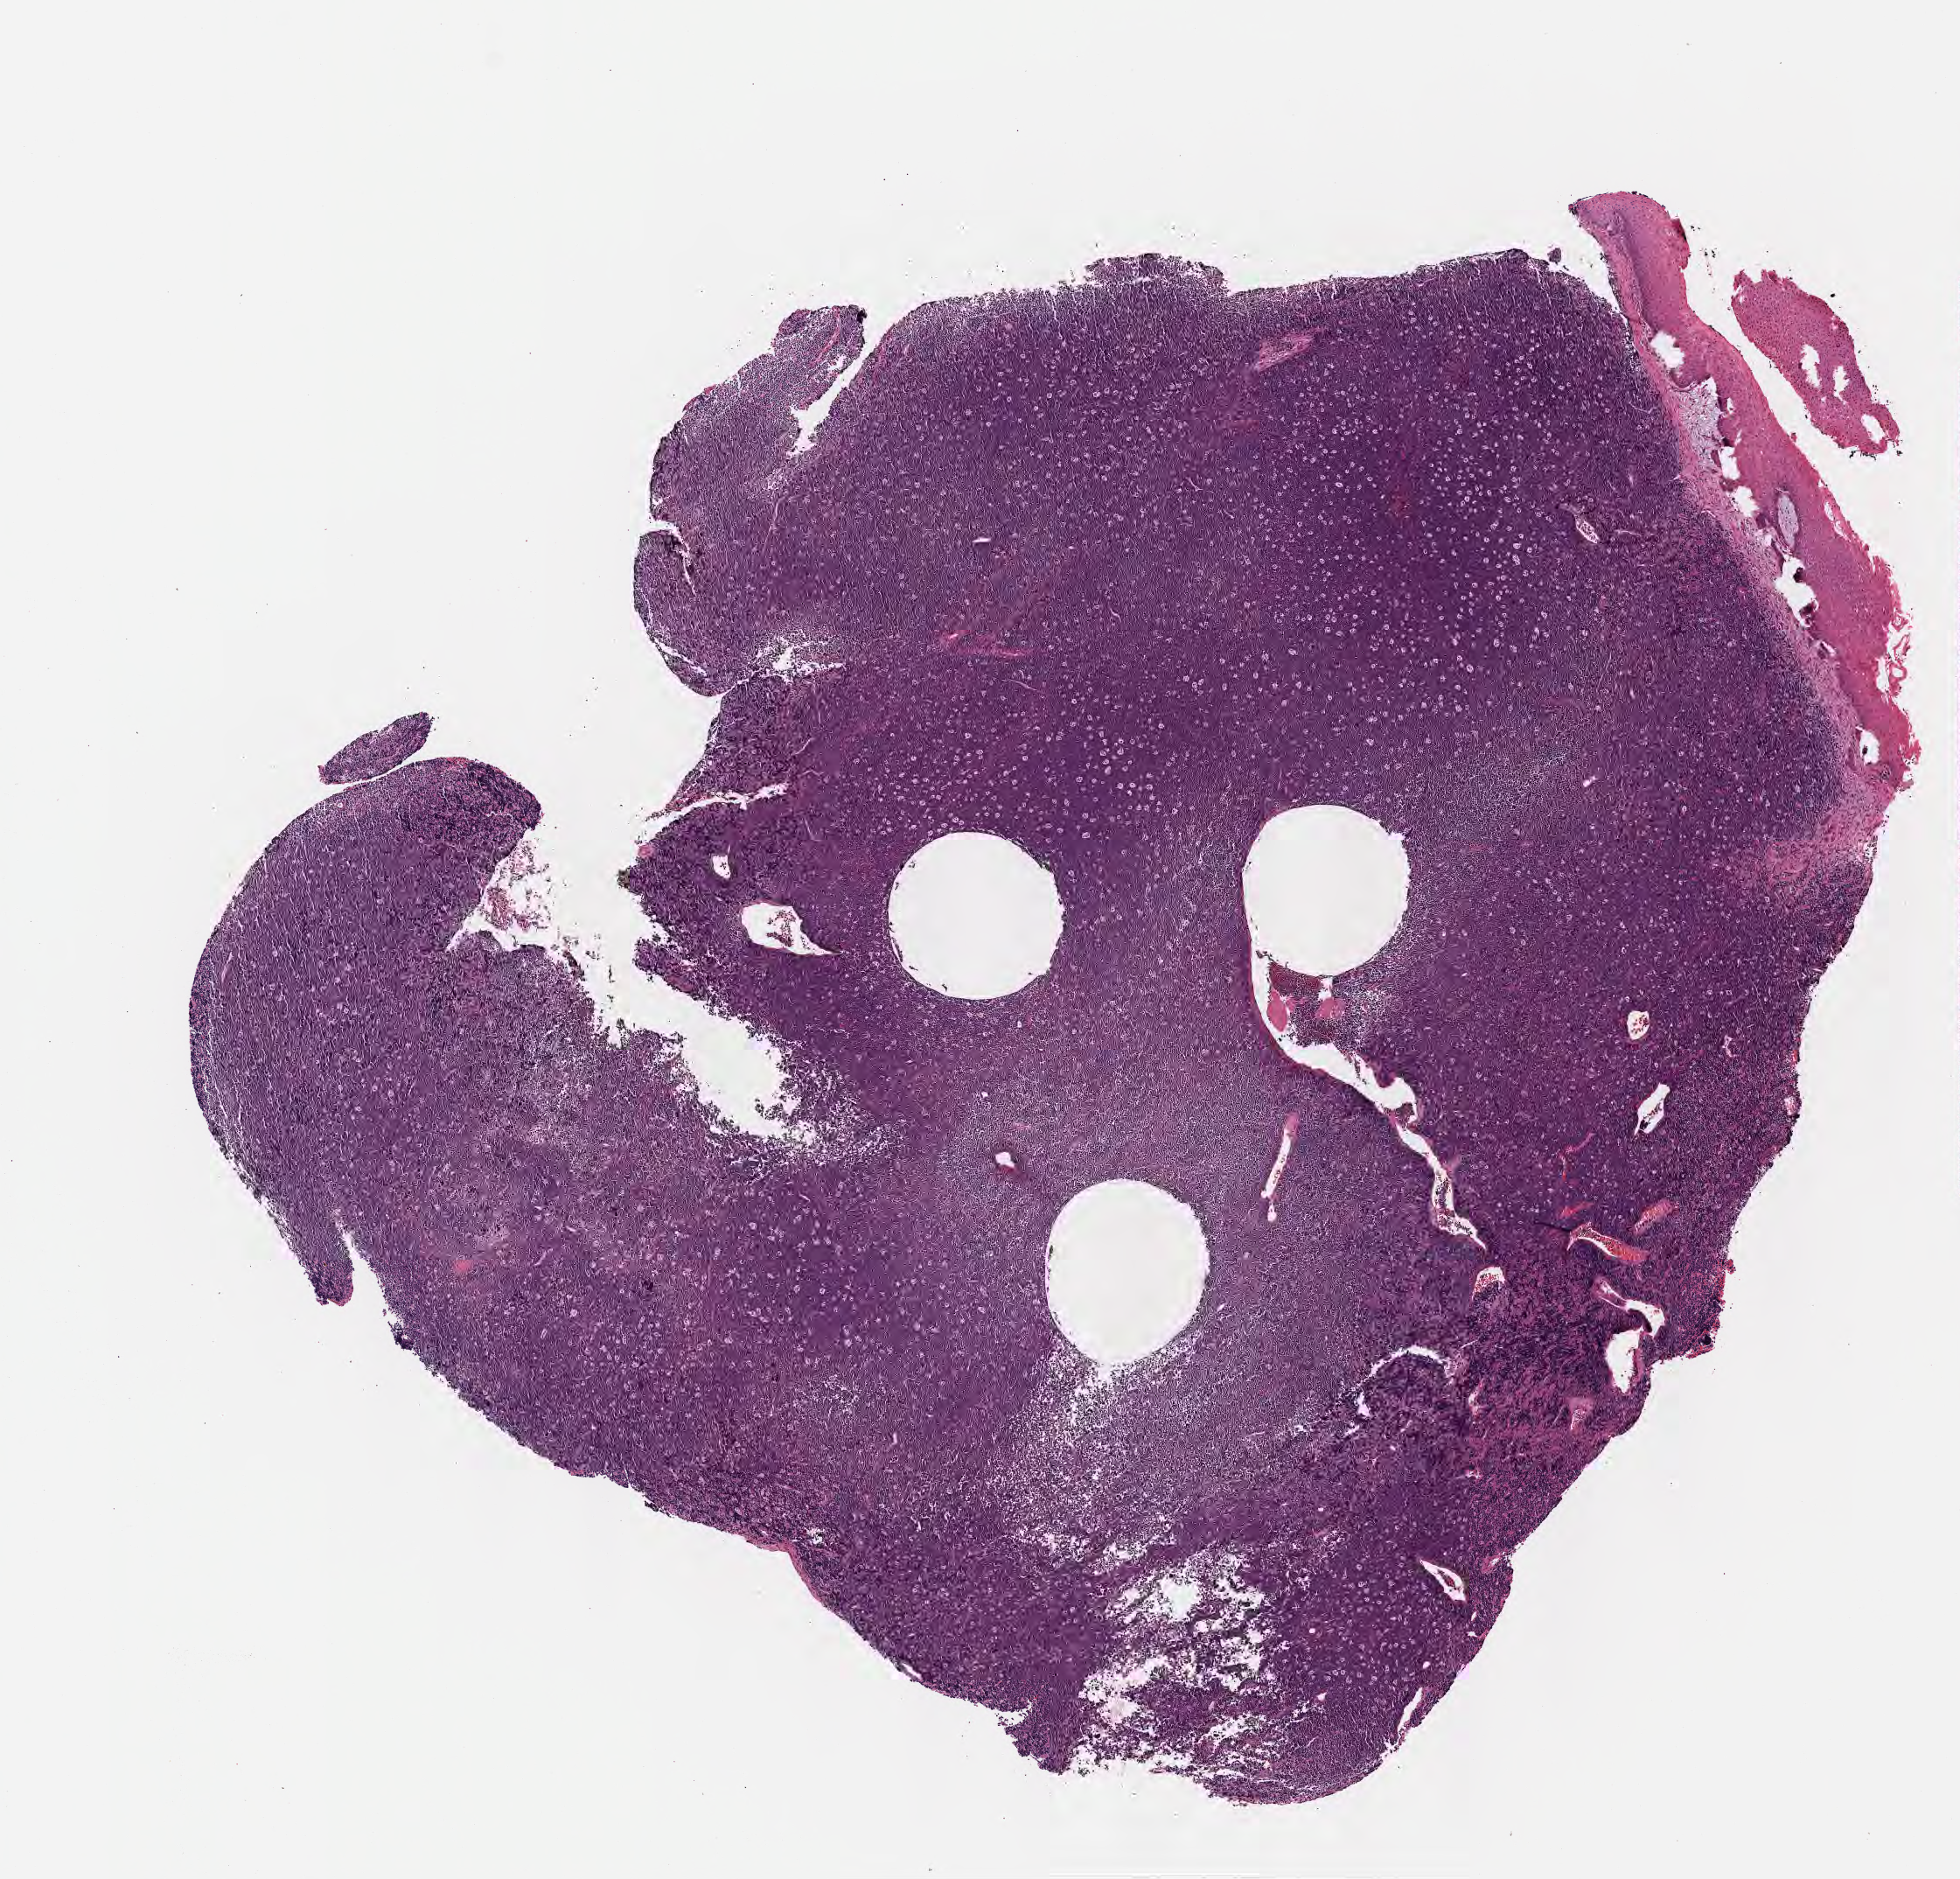
Hematoxylin and eosin (H&E) whole-slide image, low-resolution overview of the scanned area, about 9.1 x 8.7 mm. Formalin-fixed paraffin-embedded section. Primary tumor. Site: buccal mucosa. Patient: female, age at initial diagnosis 7 years. Pathologist review of this section (percent, as recorded): tumor cells 90%, tumor nuclei 95%, stromal cells 5%, necrosis 5%, normal cells 0%. Inflammatory infiltration, as recorded: lymphocyte infiltration 40%, monocyte infiltration 30%, neutrophil infiltration 5%.
* Ann Arbor stage (patient): Stage III
* section: bottom of the tissue portion
* diagnosis: Burkitt lymphoma, NOS